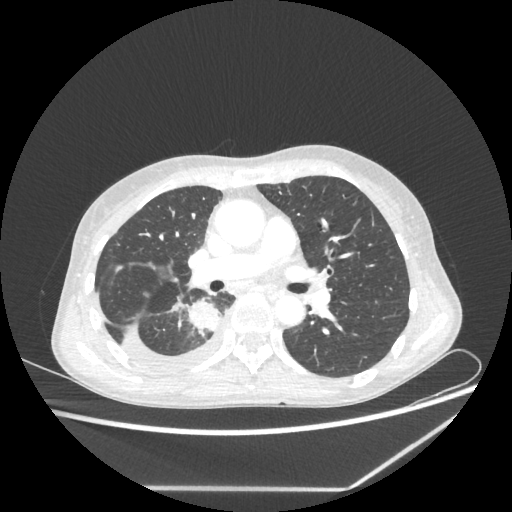
Chest CT, one axial slice; slice 132 of 237 in the series (ordered by position); reconstruction kernel STANDARD; 80 kVp; lung window (W 1500 / L -600 HU); 1.25 mm slice thickness; 512 × 512 image matrix. Patient: female, 59 years. Case-level facts recorded for this patient, not image findings: clinical TNM (as recorded): T1c N1 M1.
Annotated regions visible in this slice (rectangle marked by the reading radiologist):
- lung tumour (recorded histology: adenocarcinoma): bounding box <185,298,223,340> (left, top, right, bottom; pixels)